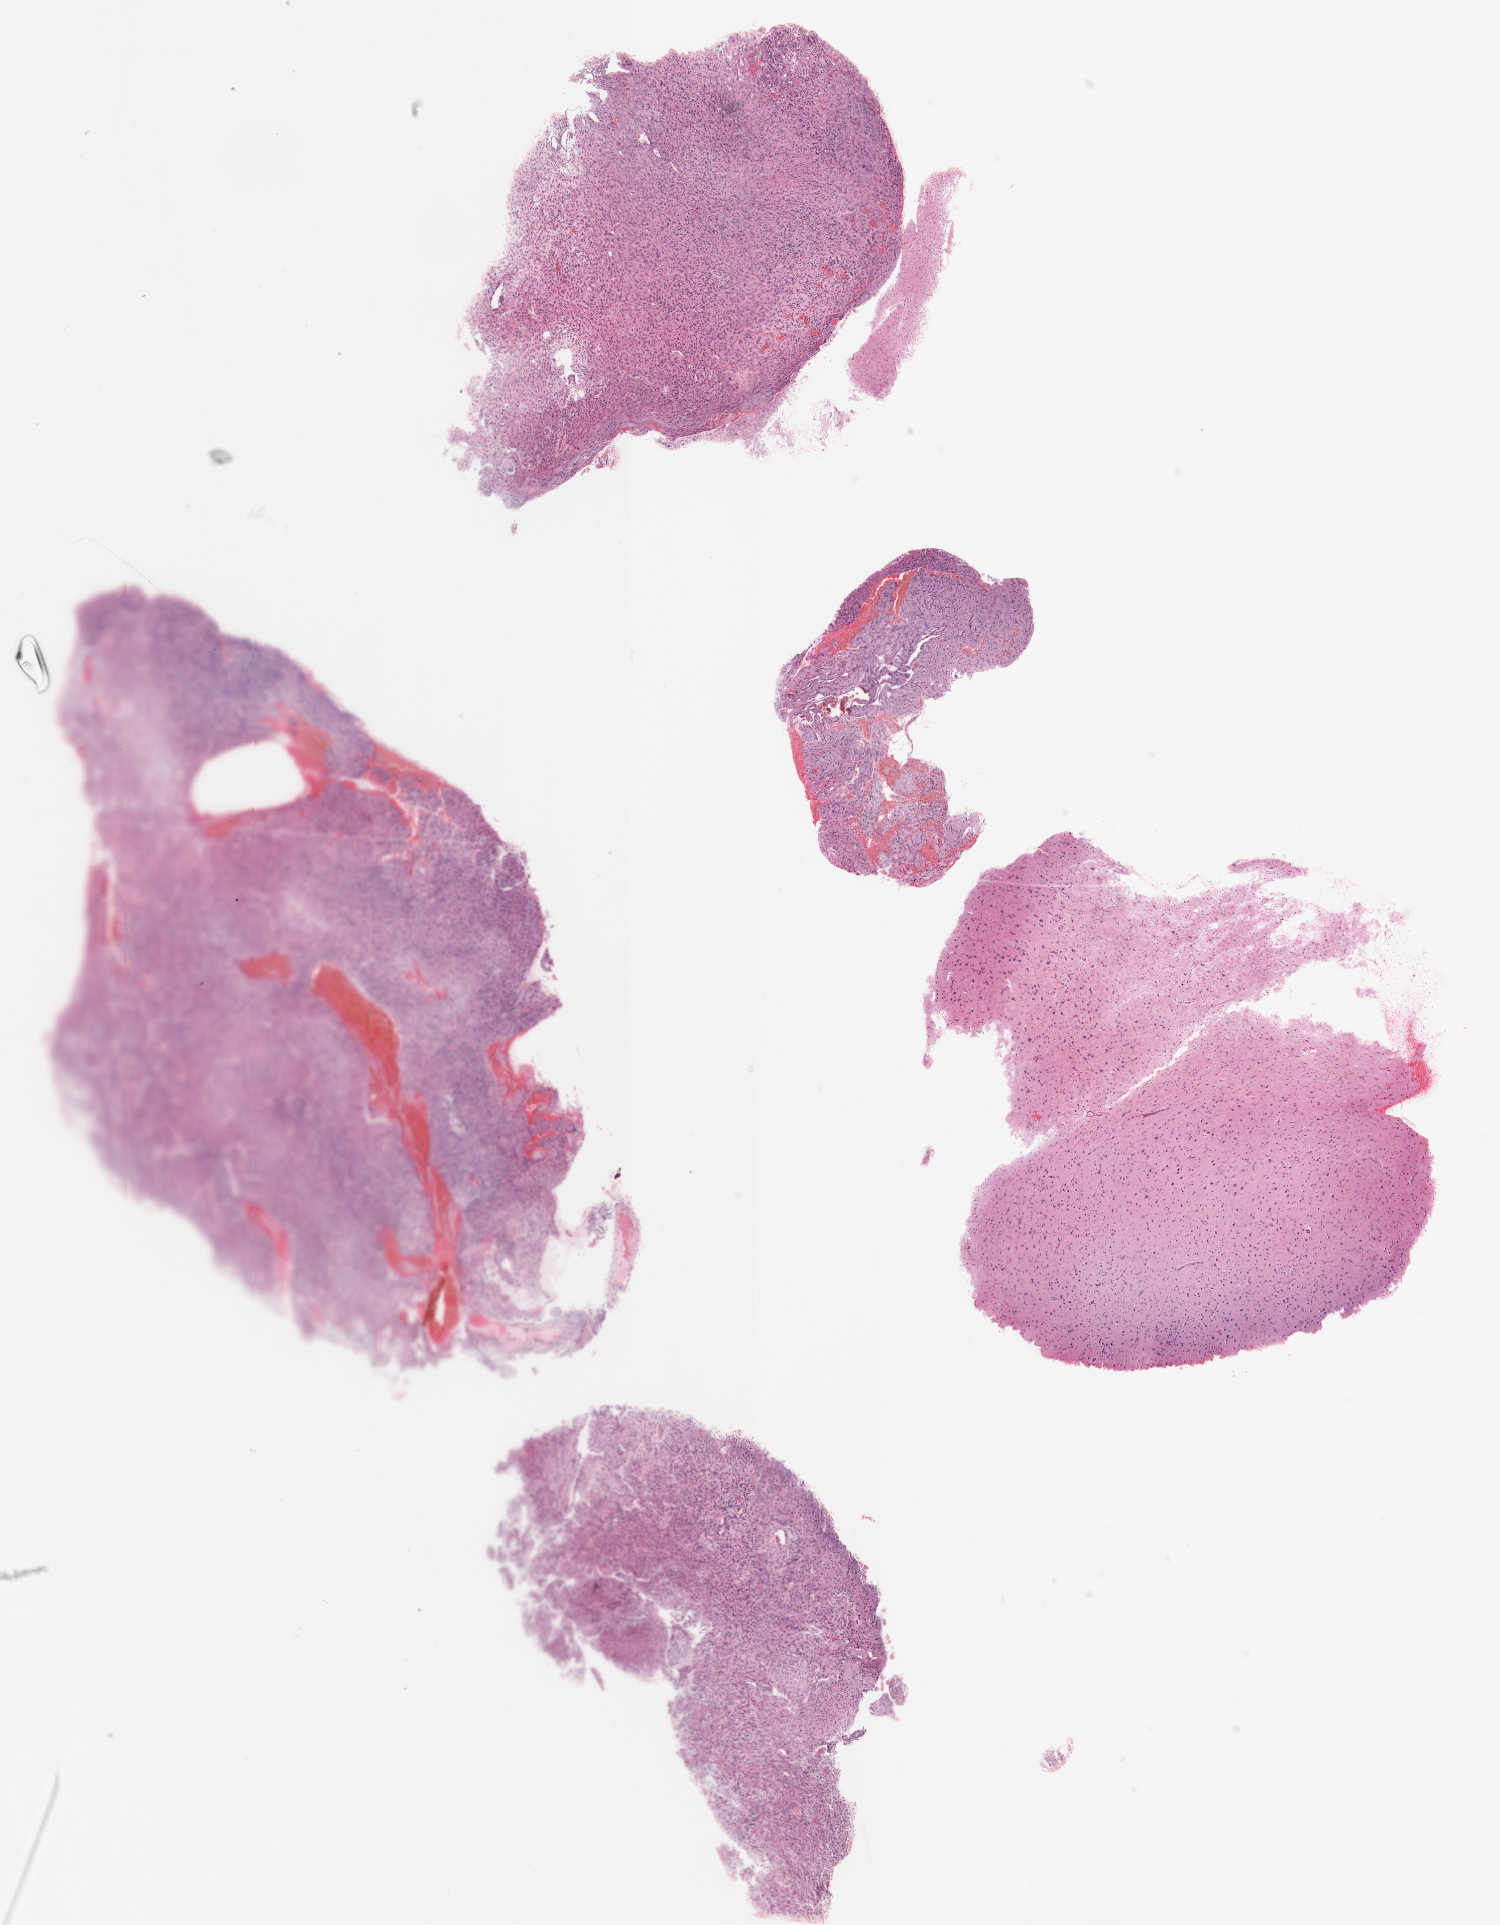
Whole-slide histology image, H&E-stained, a low-resolution overview of the entire scanned area, about 12.0 x 15.4 mm, formalin-fixed paraffin-embedded (FFPE) diagnostic section, primary tumour sample from the brain. Male, age 54 years at initial diagnosis.
Pathologic diagnosis: Glioblastoma.